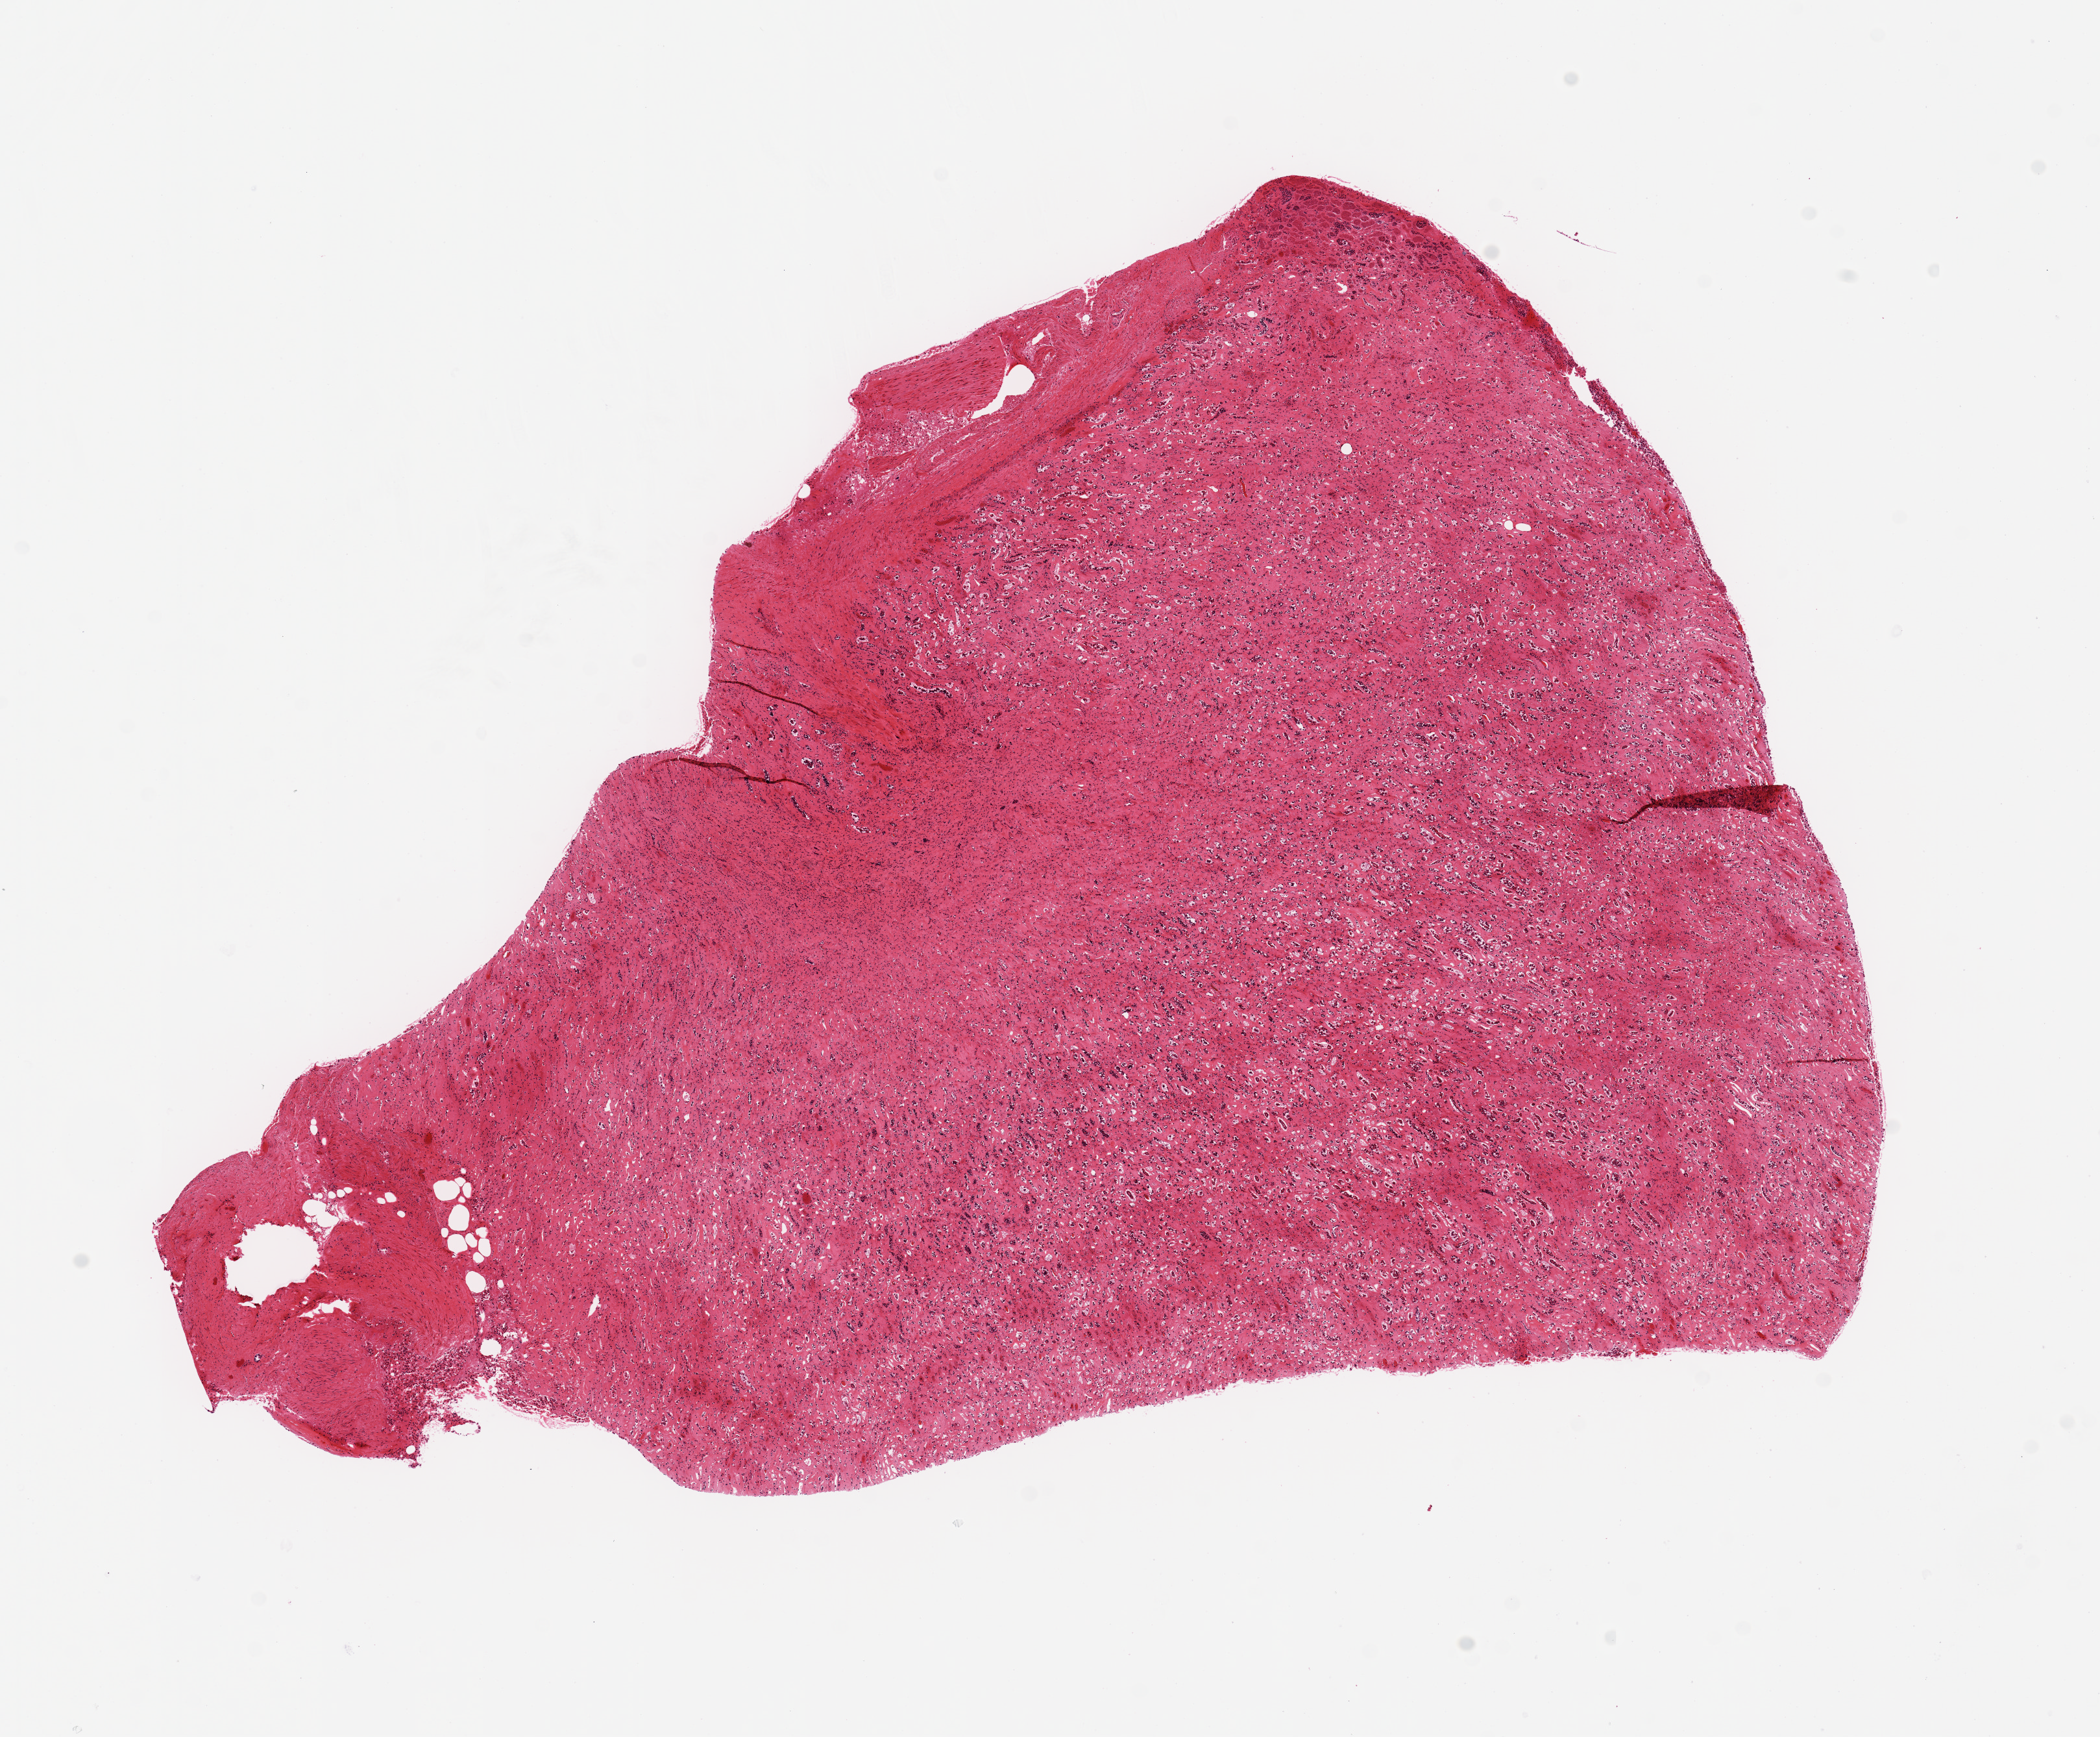
Hematoxylin and eosin (H&E) whole-slide image, a low-resolution overview of the entire scanned area, about 12.8 x 10.6 mm (from a 20x scan). PAXgene-fixed paraffin-embedded (PFPE) section. Target tissue: renal medulla. Tissue donor sample. Donor: male.
Review note (as recorded): 10x6 mm.Moderate fibrosis and autolysis.